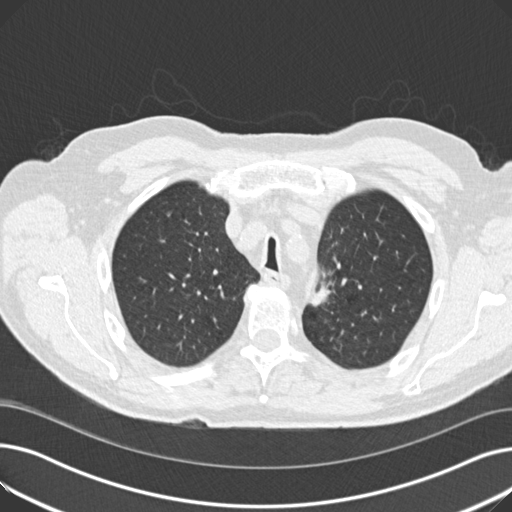
Chest CT (low-dose screening protocol), one axial image, third annual screen, lung window (W 1500 / L -600 HU), 2 mm slice thickness, slice 48 of 191 in the series, 512 × 512 image matrix, field of view 370 × 370 mm. Male participant, aged 70 years at enrolment.
Lesion marked by an expert reader, bounding box <304,265,343,310> (left, top, right, bottom; pixels). The screening reader recorded 2 non-calcified nodules or masses ≥4 mm on this exam (left upper lobe, left lower lobe); which of them this box marks is not recorded. Lung cancer was diagnosed 175 days after this screen: mixed cell adenocarcinoma, left upper lobe, poorly differentiated (G3), stage IIB (AJCC 6th edition), 17 mm at pathology.